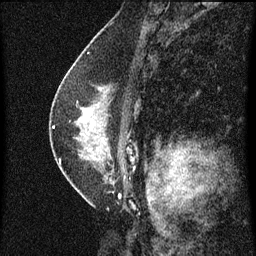
Breast MRI (dynamic contrast-enhanced), one sagittal slice; position 37 of 60 along the scan axis; dynamic contrast-enhanced series, image 2 of 3 at this slice position (ordered by acquisition); 1.5 T; TE 4.2 ms, TR 8 ms; 2 mm slice thickness; 256 × 256 image matrix, field of view 180 × 180 mm. Female patient, age 47 years.
Annotated regions visible in this slice (semi-automatically segmented with operator editing):
- analysis volume of interest (the breast-tissue region the enhancement analysis was run in; not a lesion): bounding box <54,80,136,187> (left, top, right, bottom; pixels)
- tumour enhancement mask (voxels above the 70 % enhancement threshold inside the analysis volume of interest): <54,126,61,161>